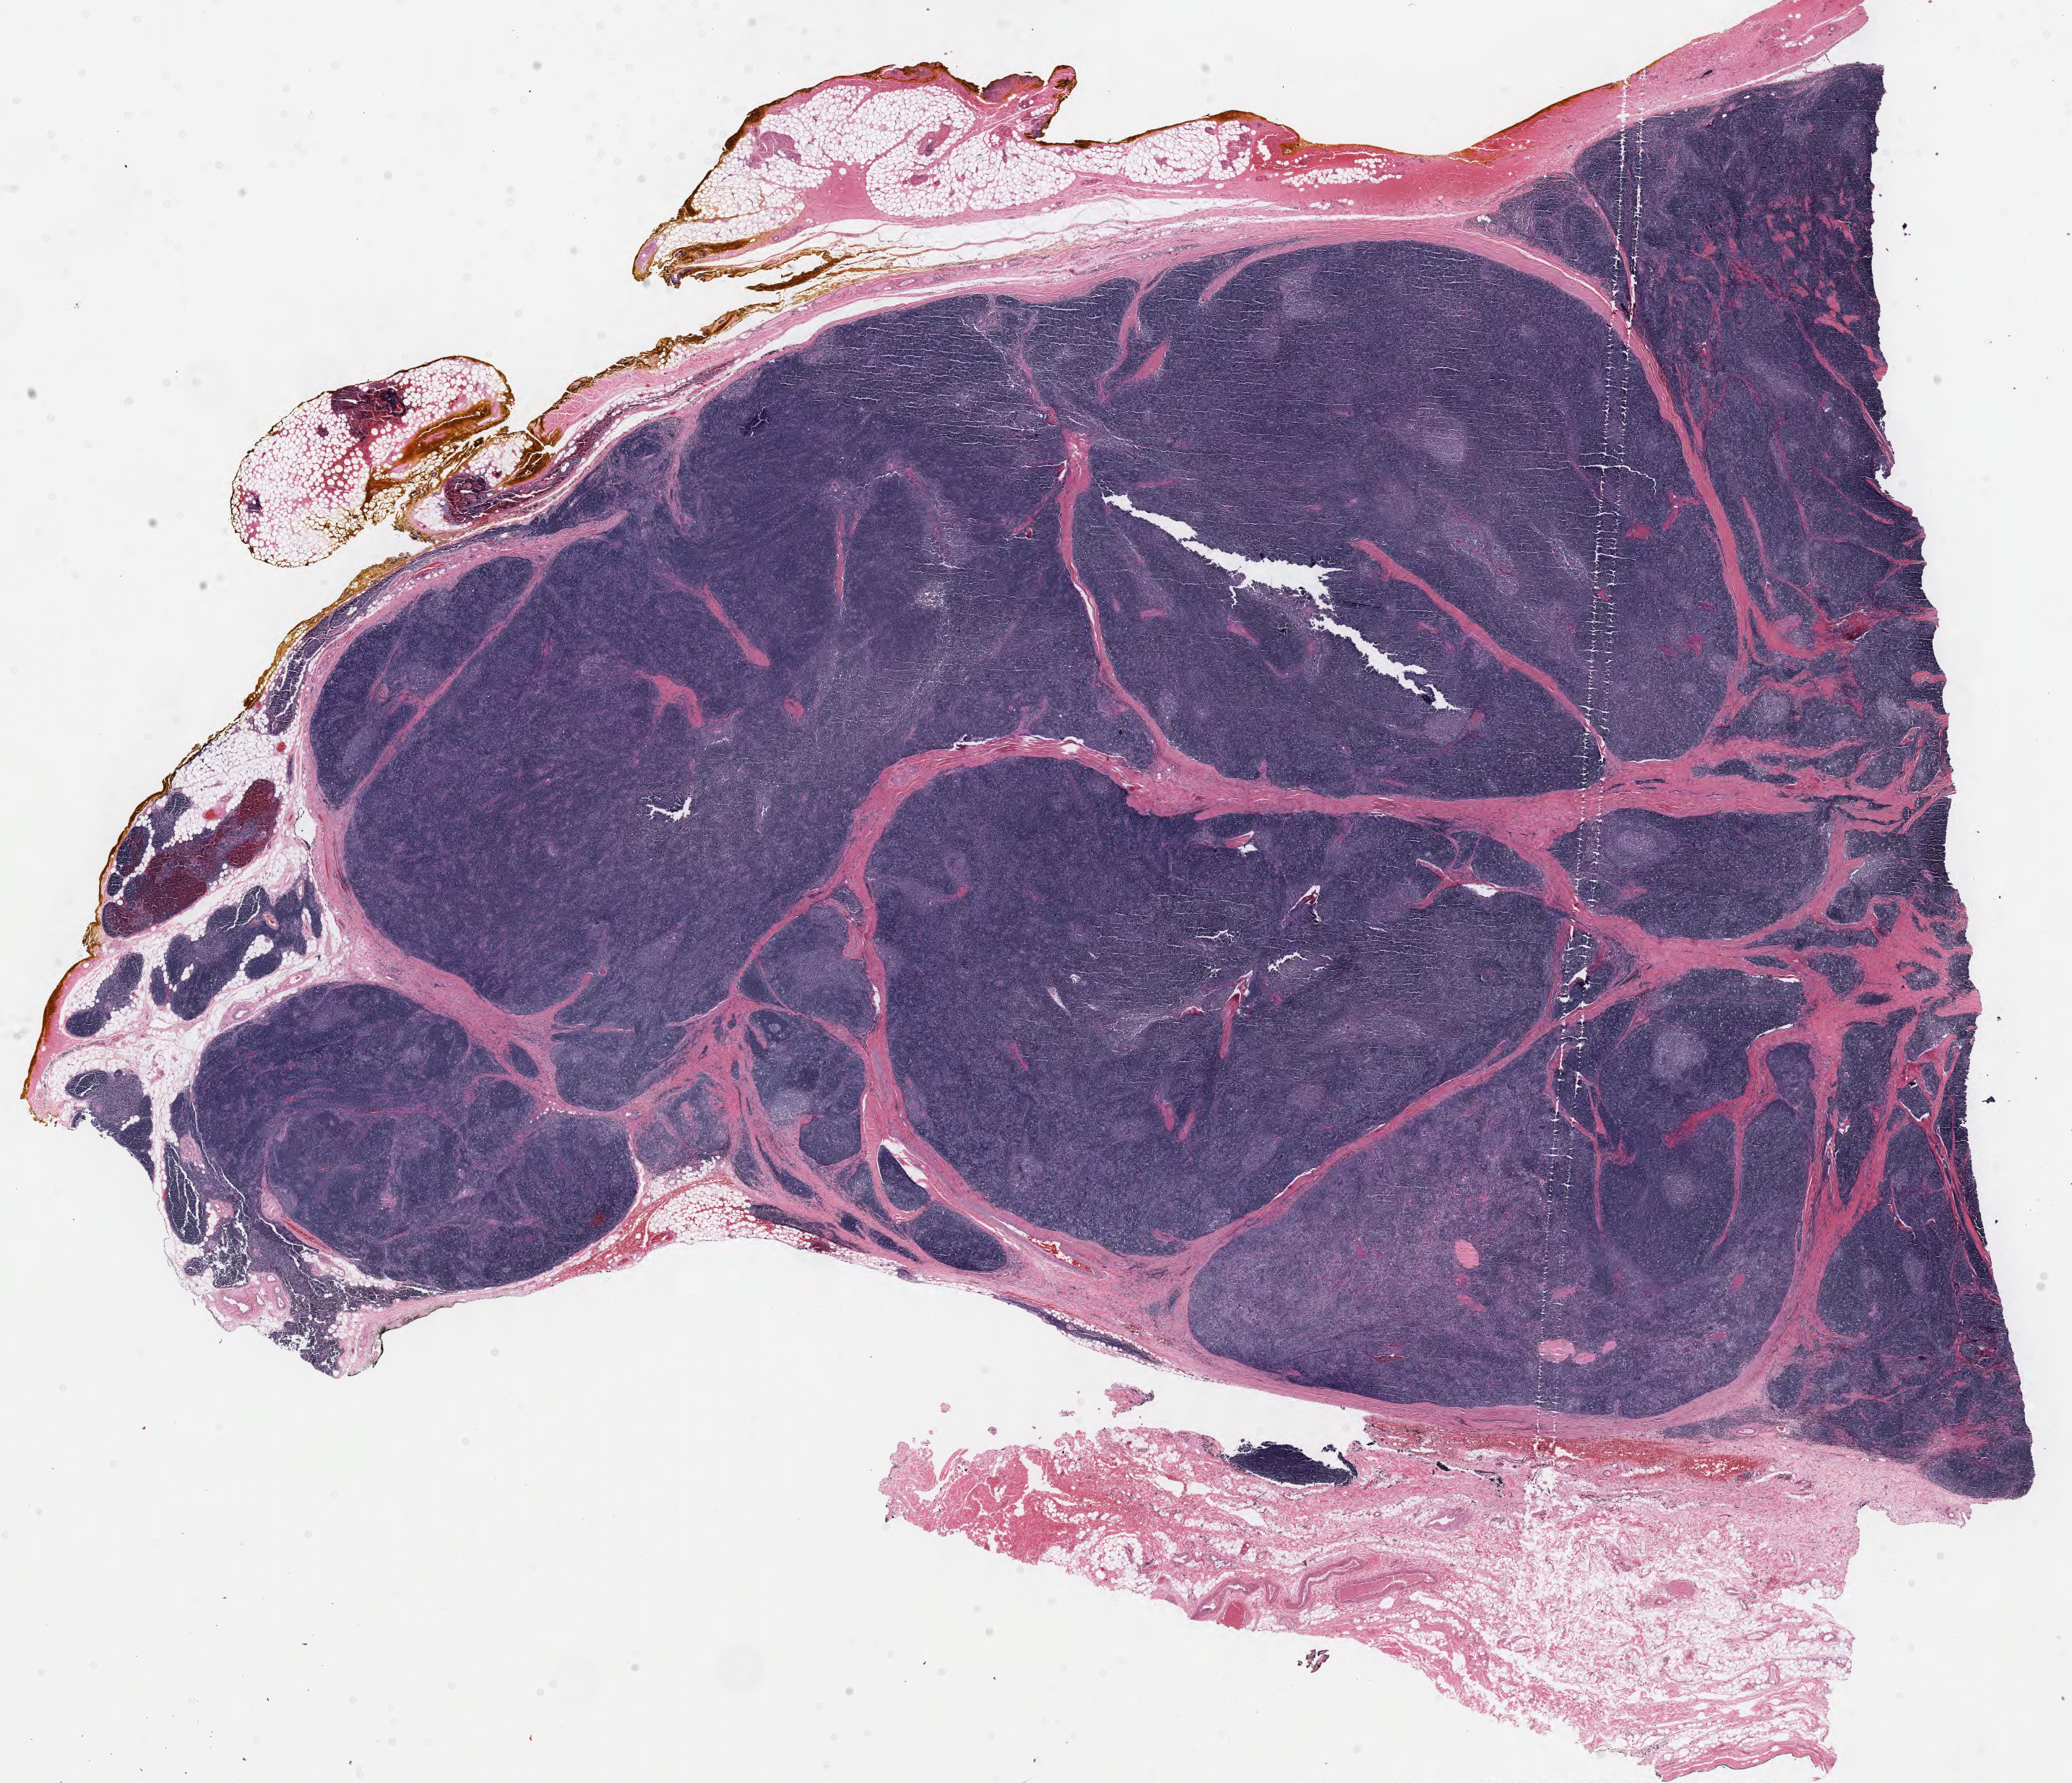
Digitized H&E tissue section (whole slide), whole scanned area (about 22.7 x 19.6 mm) shown as a low-resolution overview. FFPE section. Primary tumour sample from the thymus. Patient: female, age at initial diagnosis 57 years.
Histologic diagnosis: Thymoma, type B1, NOS.